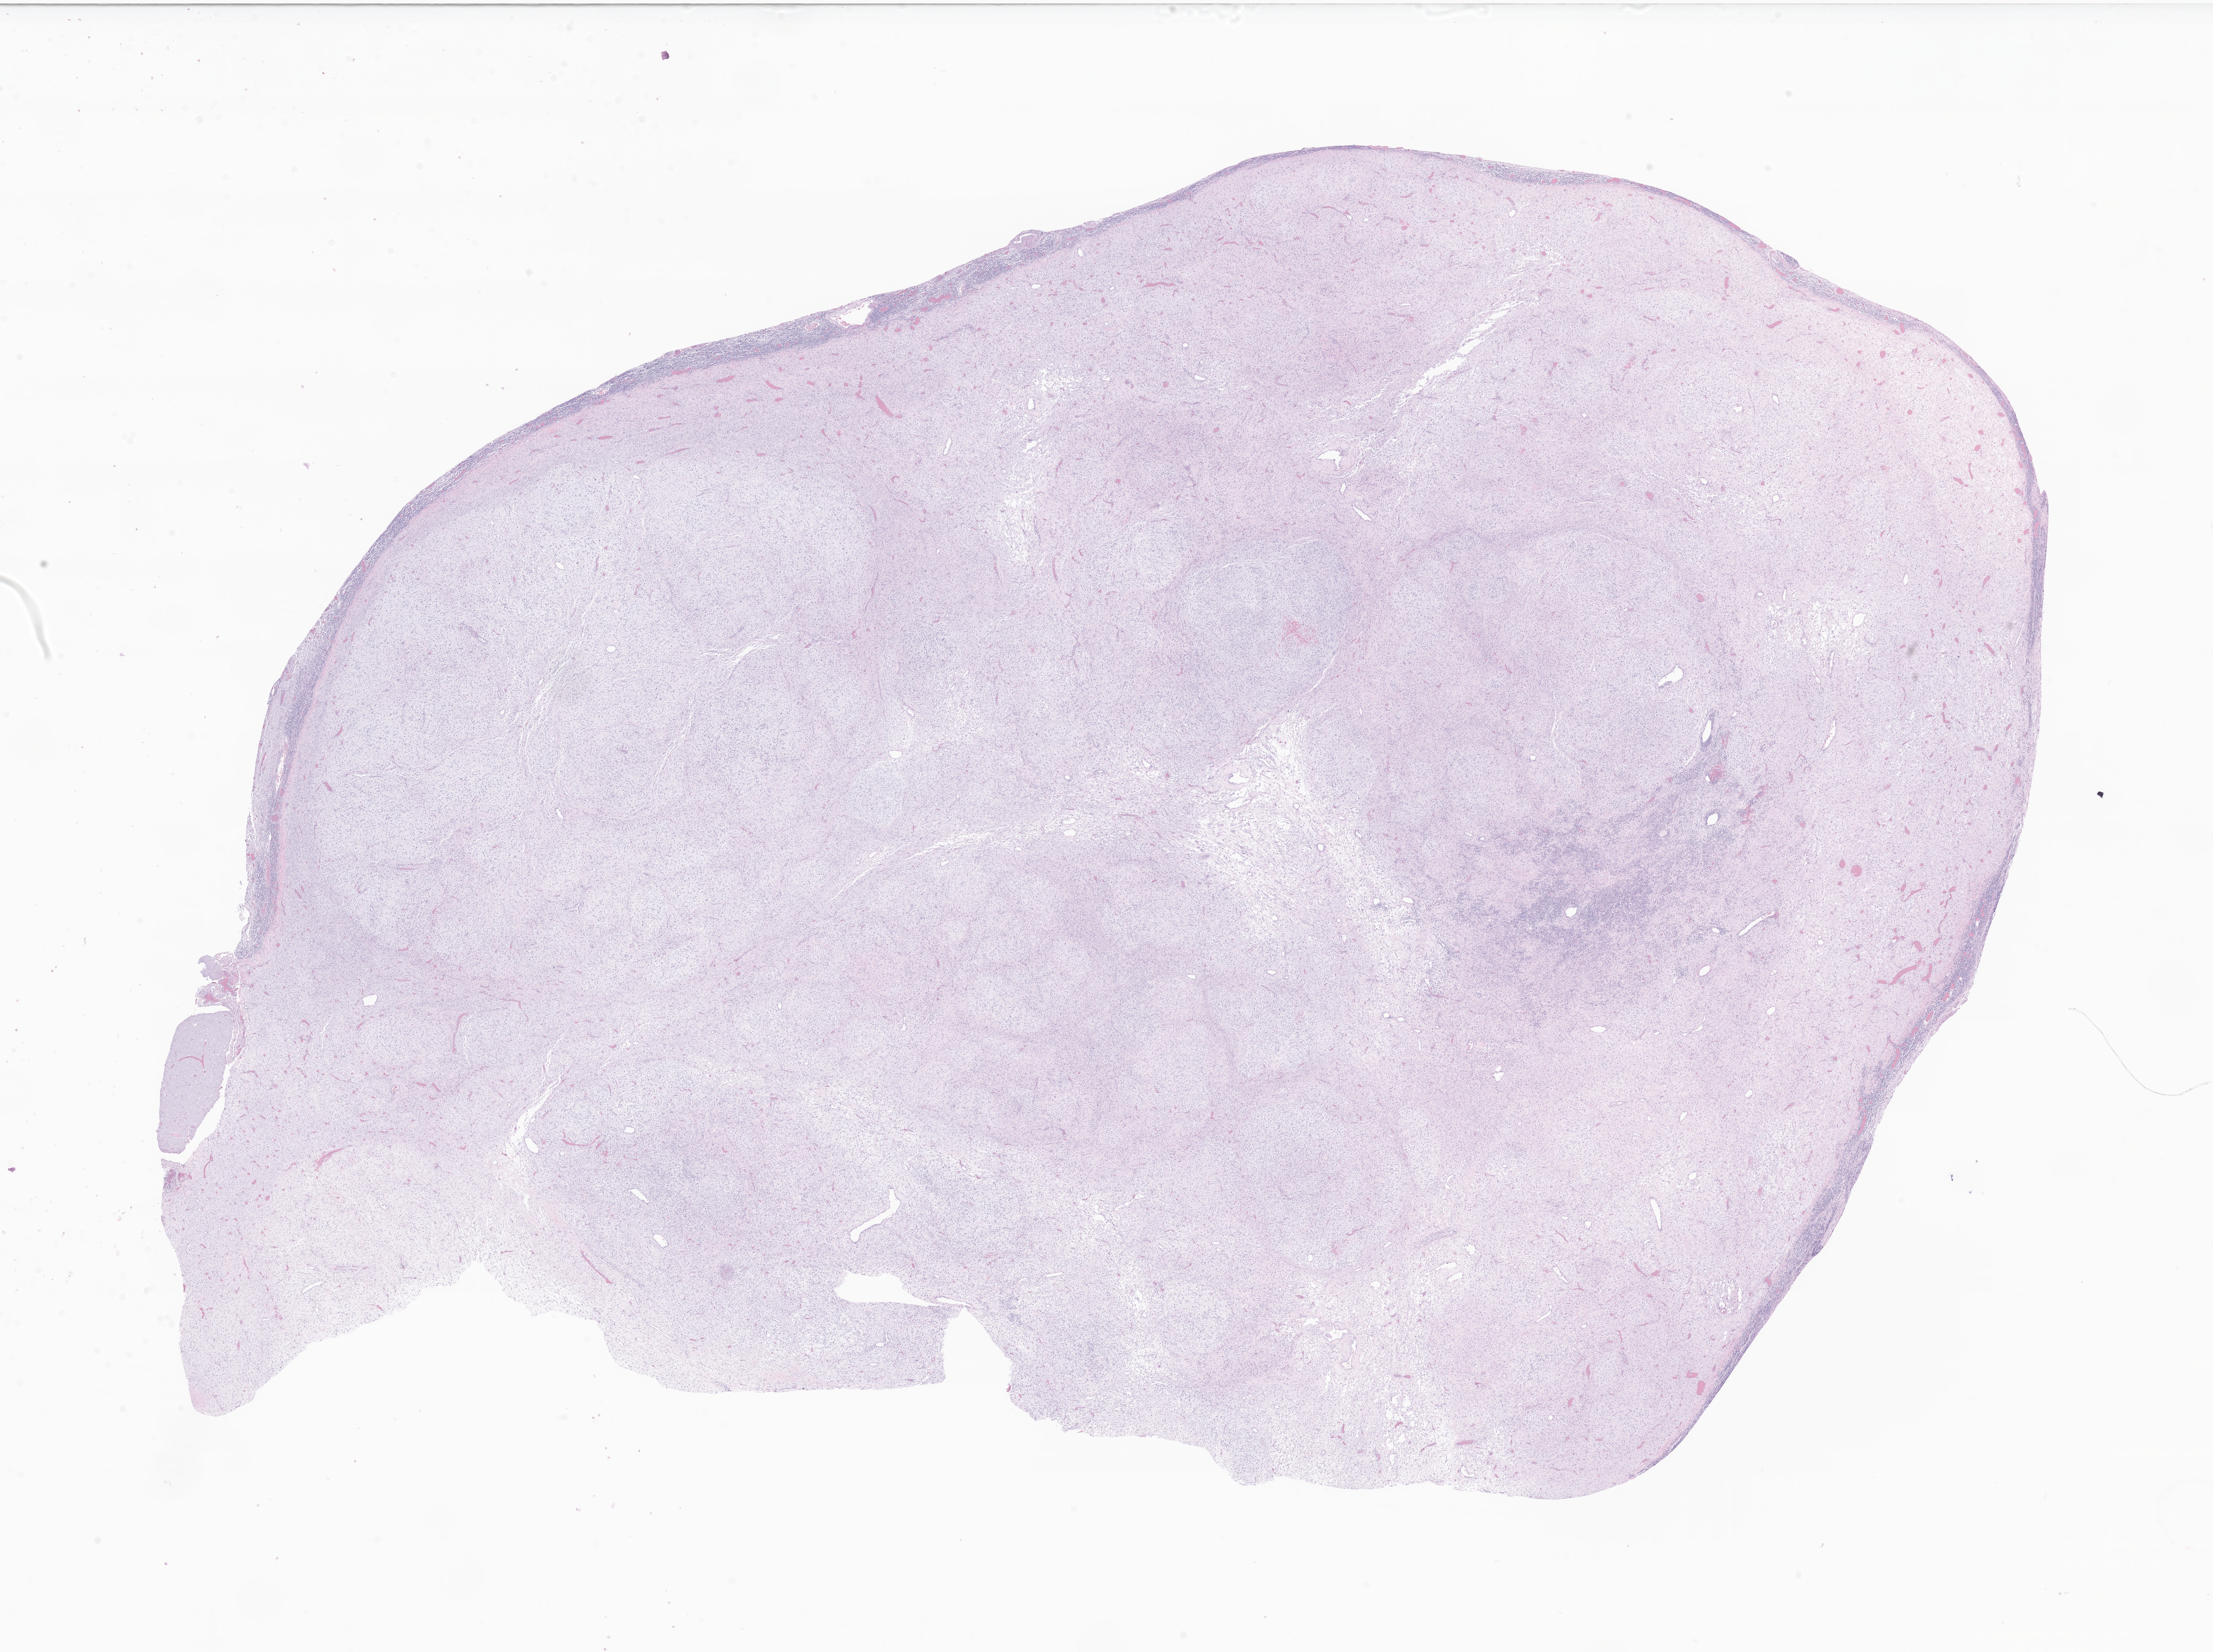
H&E whole-slide image of tumor tissue from the frontal lobe, a low-resolution overview of the entire scanned area, about 26.0 x 19.5 mm; formalin-fixed, paraffin-embedded (FFPE) tissue. Patient female; age 180 months.
- diagnosis: Mesenchymal chondrosarcoma